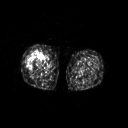
FDG PET of an extremity soft-tissue mass (from a PET/CT study), one axial slice. Slice 222 of 311 in the series (ordered by position). 3.27 mm slice thickness. 128 × 128 image matrix. Patient: female, 57 years. From the clinical record (not read from this slice): histological type: pleiomorphic undifferentiated sarcoma; grade: high; site of the primary tumour: right quadricep.
Structures marked on this image (expert contour drawn on MRI and transferred to this co-registered scan by the dataset authors):
- tumour plus oedema (research contour): bounding box [x1, y1, x2, y2] px = [26, 50, 41, 68]